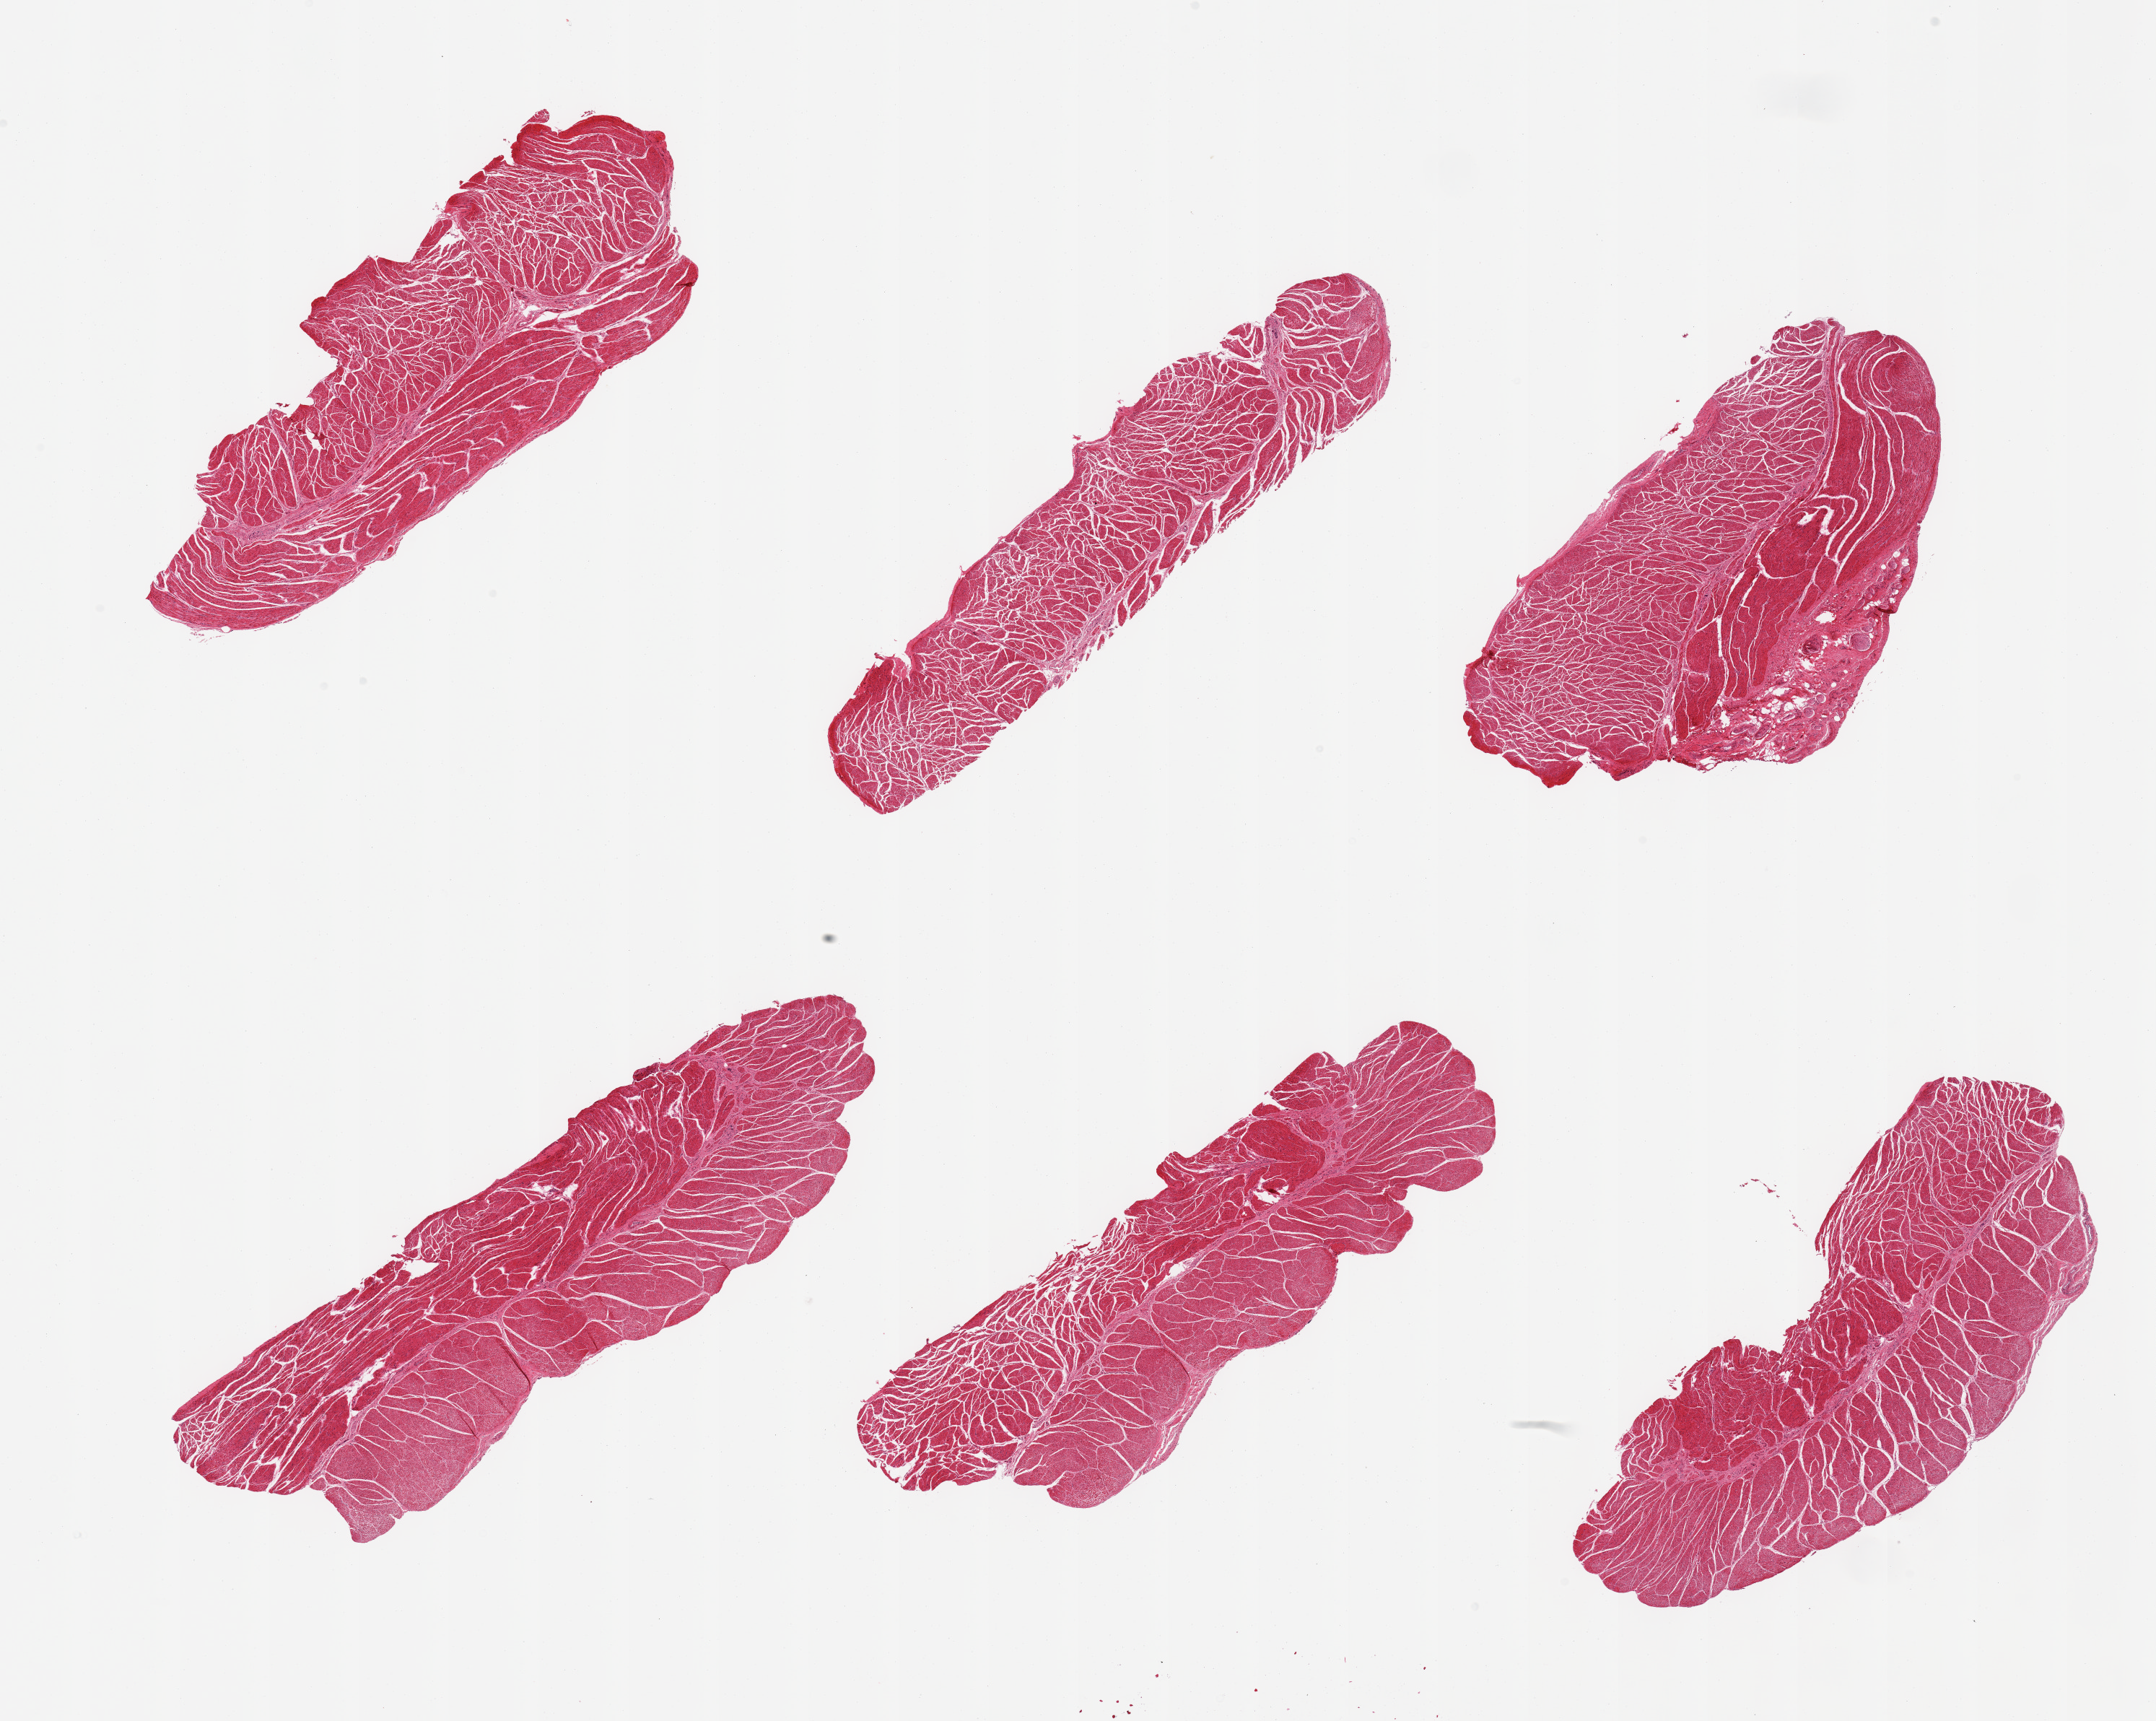
Digitized H&E-stained section, brightfield, shown as a low-resolution overview of the whole scanned area (about 23.6 x 18.9 mm, slide scanned at 20x), PAXgene-fixed, paraffin-embedded tissue, section of esophageal muscle (target tissue), donor tissue sample. Donor: female.
Review note (as recorded): 6 pieces; well dissected: pure muscle.